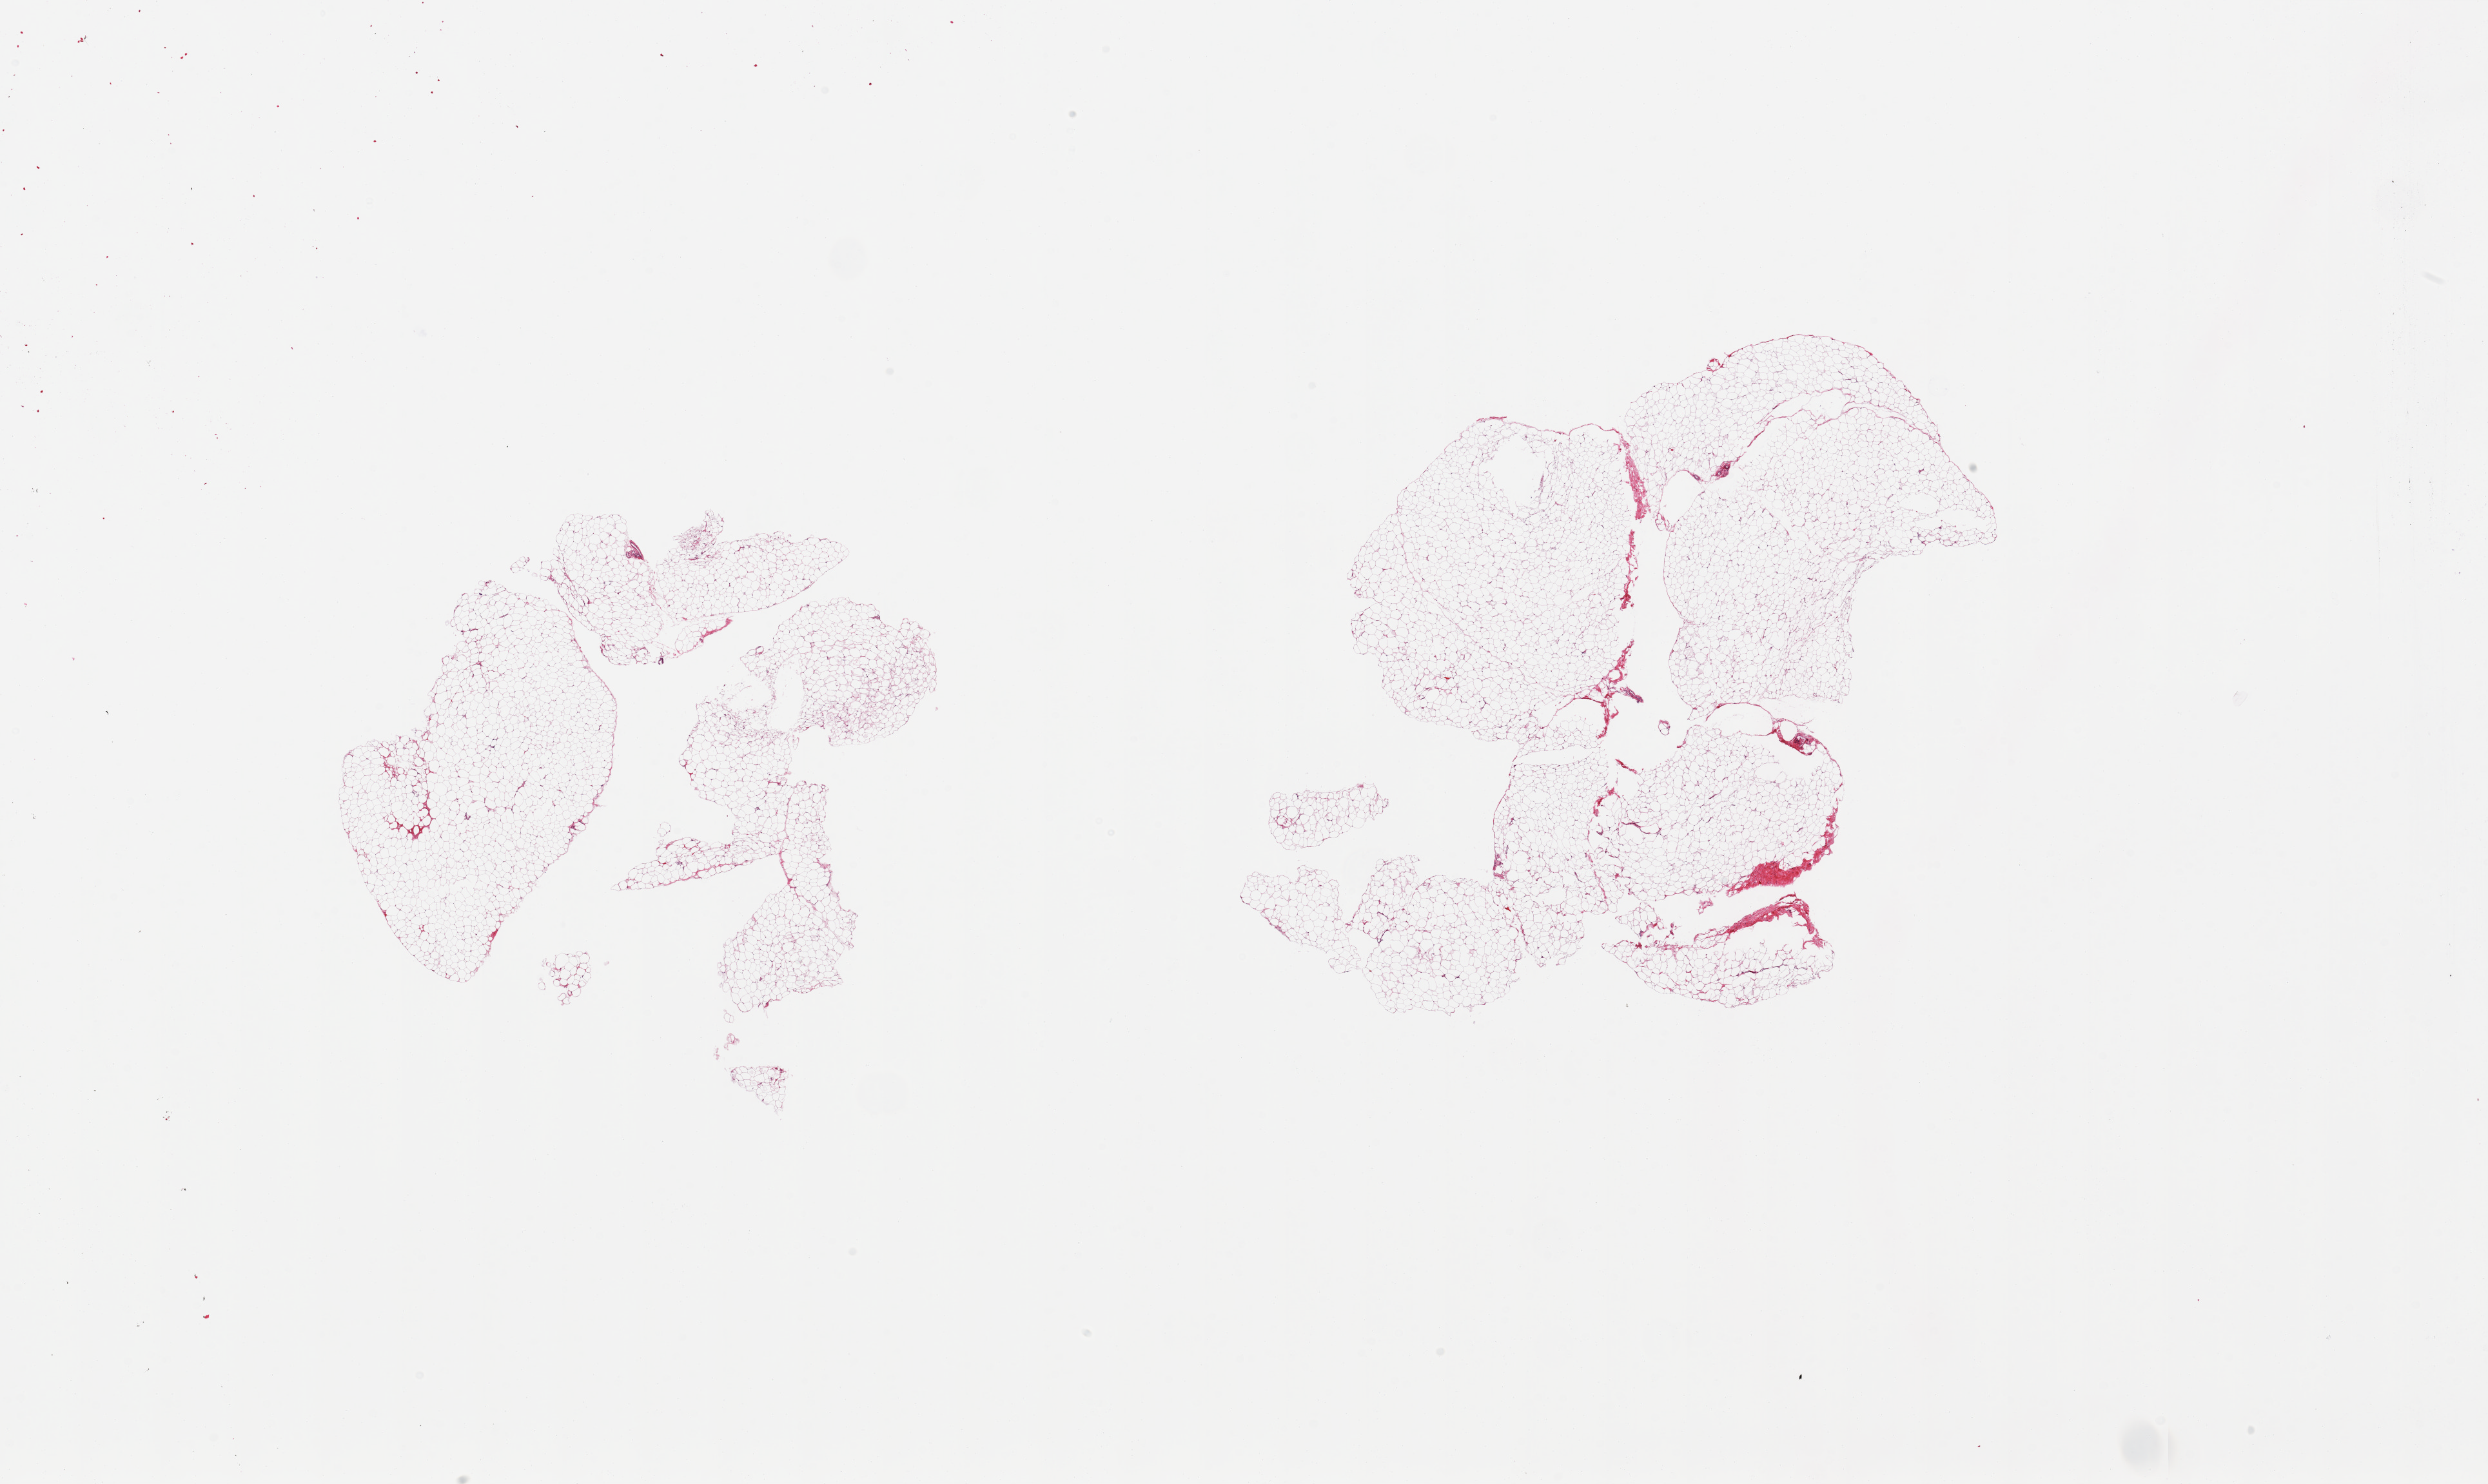
Whole-slide image, H&E stain, brightfield, low-resolution overview of the scanned area, about 30.5 x 18.2 mm (acquisition: 20x scan); PAXgene-fixed, paraffin-embedded tissue; section of breast (target tissue); tissue donor sample.
Pathologist's review note for this sample: 2 pieces, adipose elements only.